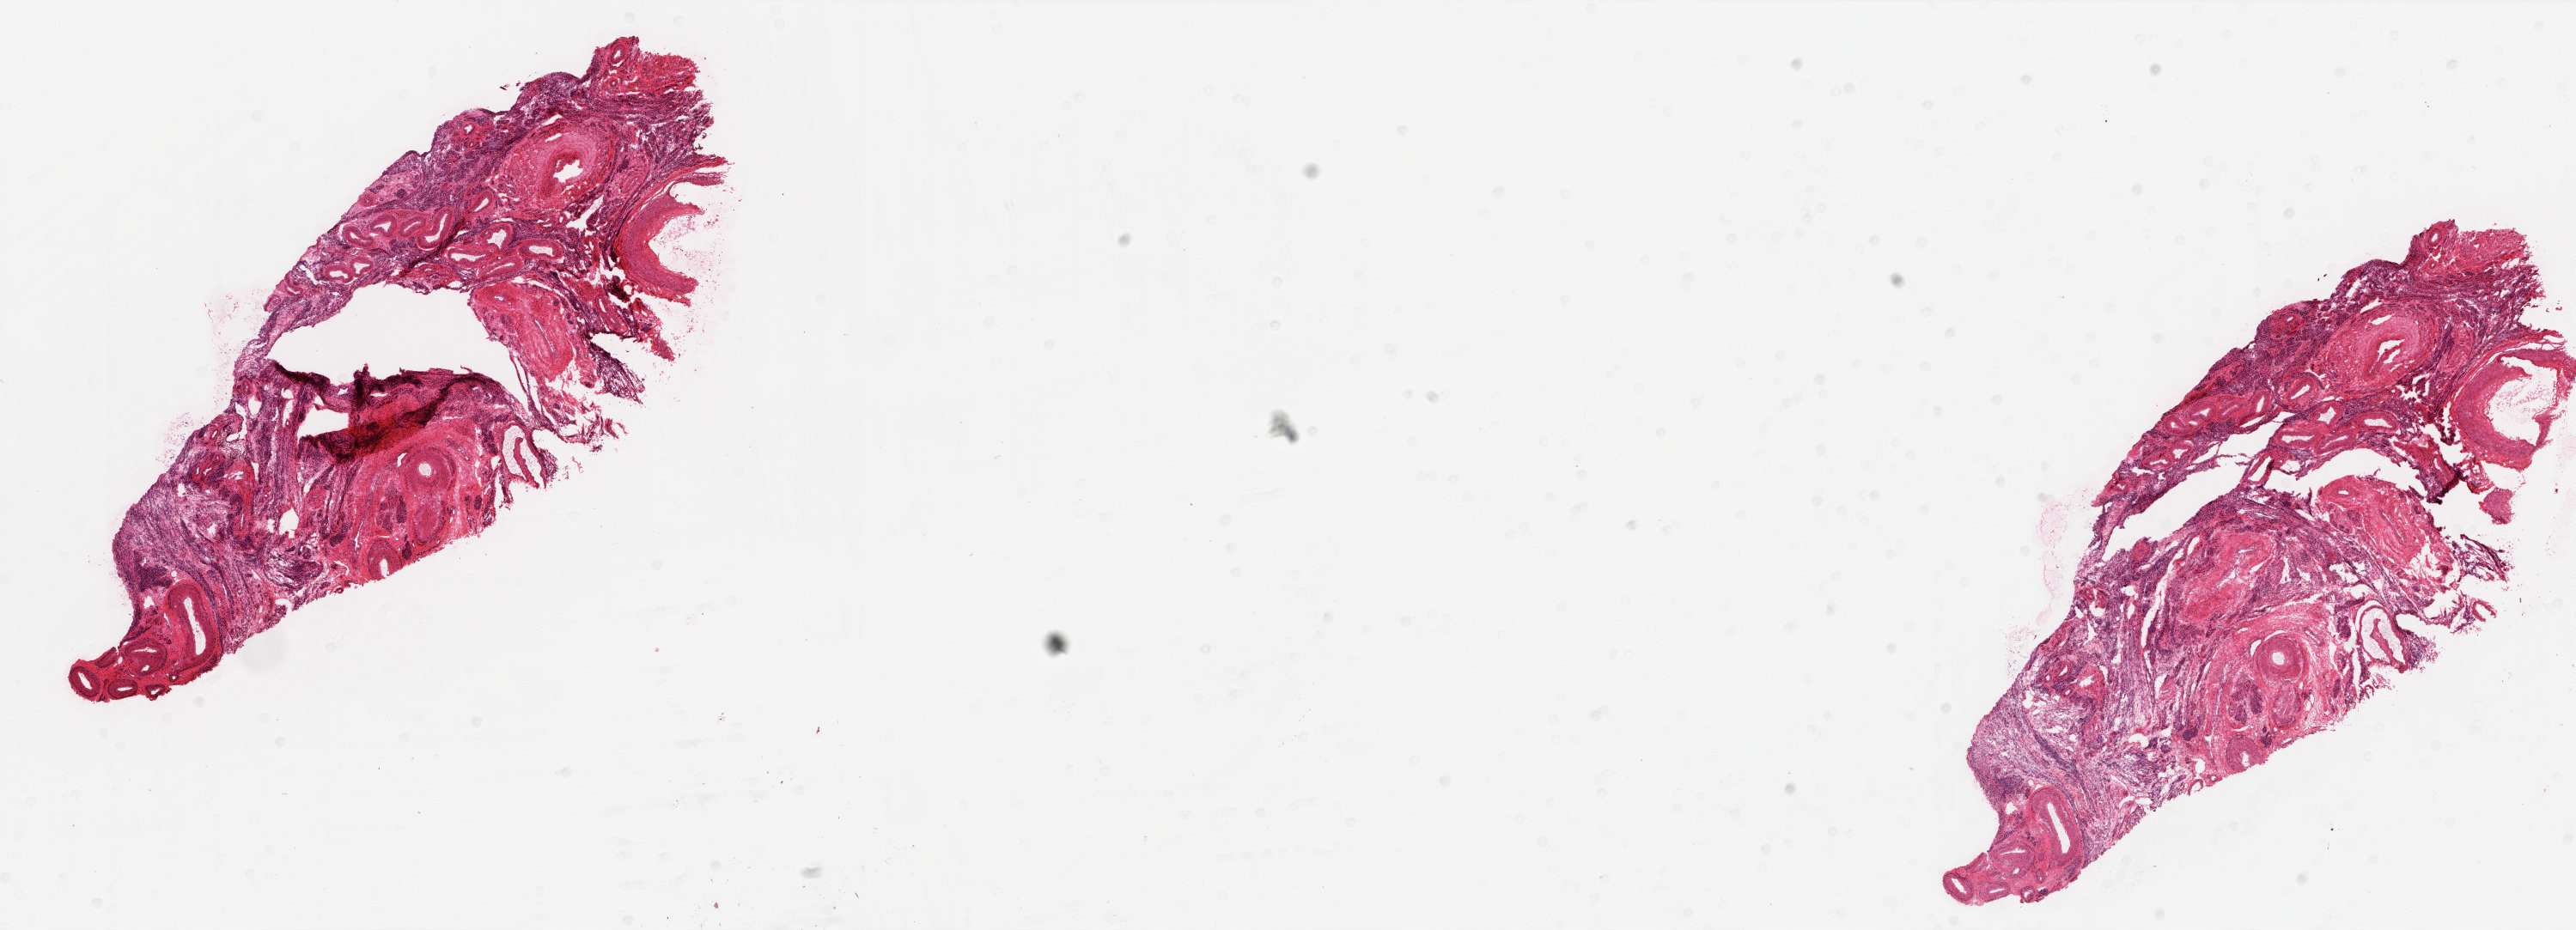
Whole-slide histology image, Hematoxylin and eosin (H&E) stained — low-resolution overview of the scanned area, about 24.0 x 8.6 mm (from a 20x scan); frozen section; solid tissue normal (non-tumour tissue) sample from the ovary. Female, age 79 years at initial diagnosis.
- this section: solid tissue normal (non-tumour) sample from the same patient
- patient diagnosis: Serous cystadenocarcinoma, NOS